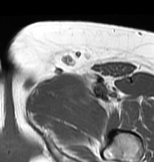
MRI of an extremity soft-tissue mass, one axial slice; slice 47 of 83 in the series (ordered by position); MR volume resampled by the dataset authors to the PET/CT grid (not the native acquisition matrix); 154 × 162 image matrix, field of view 150 × 158 mm. Female patient. From the clinical record (not read from this slice): histological type: myxofibrosarcoma; grade: intermediate; site of the primary tumour: left thigh.
Annotated regions visible in this slice (expert contour drawn on MRI and transferred to this co-registered scan by the dataset authors):
- gross tumour volume including surrounding oedema: bounding box (x1, y1, x2, y2) in pixels: (24, 71, 125, 115)